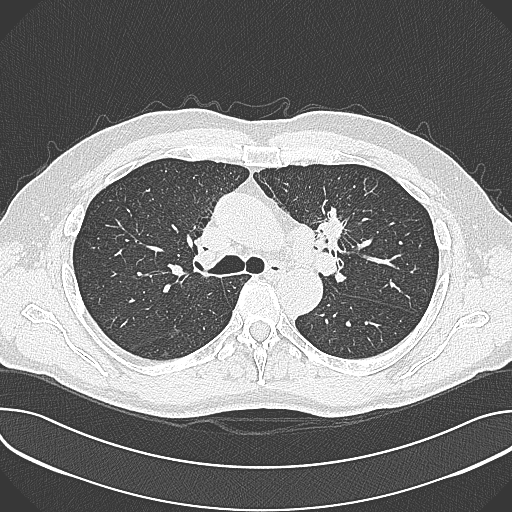
Axial slice from a low-dose chest CT screening exam, baseline screening round, lung window (W 1500 / L -600 HU), slice 111 of 361 in the series, 512 × 512 image matrix, field of view 380 × 380 mm. Male participant, aged 59 years at enrolment. Current smoker at enrolment.
• Expert-annotated lung lesion, bounding box [x1, y1, x2, y2] px = [303, 194, 364, 256].
• The screening reader recorded 2 non-calcified nodules or masses ≥4 mm on this exam (left upper lobe, left upper lobe); which of them this box marks is not recorded.
• Official screen result: positive, change unspecified: nodule(s) >= 4 mm or enlarging nodule(s), mass(es), or other non-specific abnormalities suspicious for lung cancer.
• Participant outcome: lung cancer diagnosed 21 days after this screen — non-small cell carcinoma, left upper lobe, poorly differentiated (G3), stage IIIA (AJCC 6th edition), 35 mm at pathology.